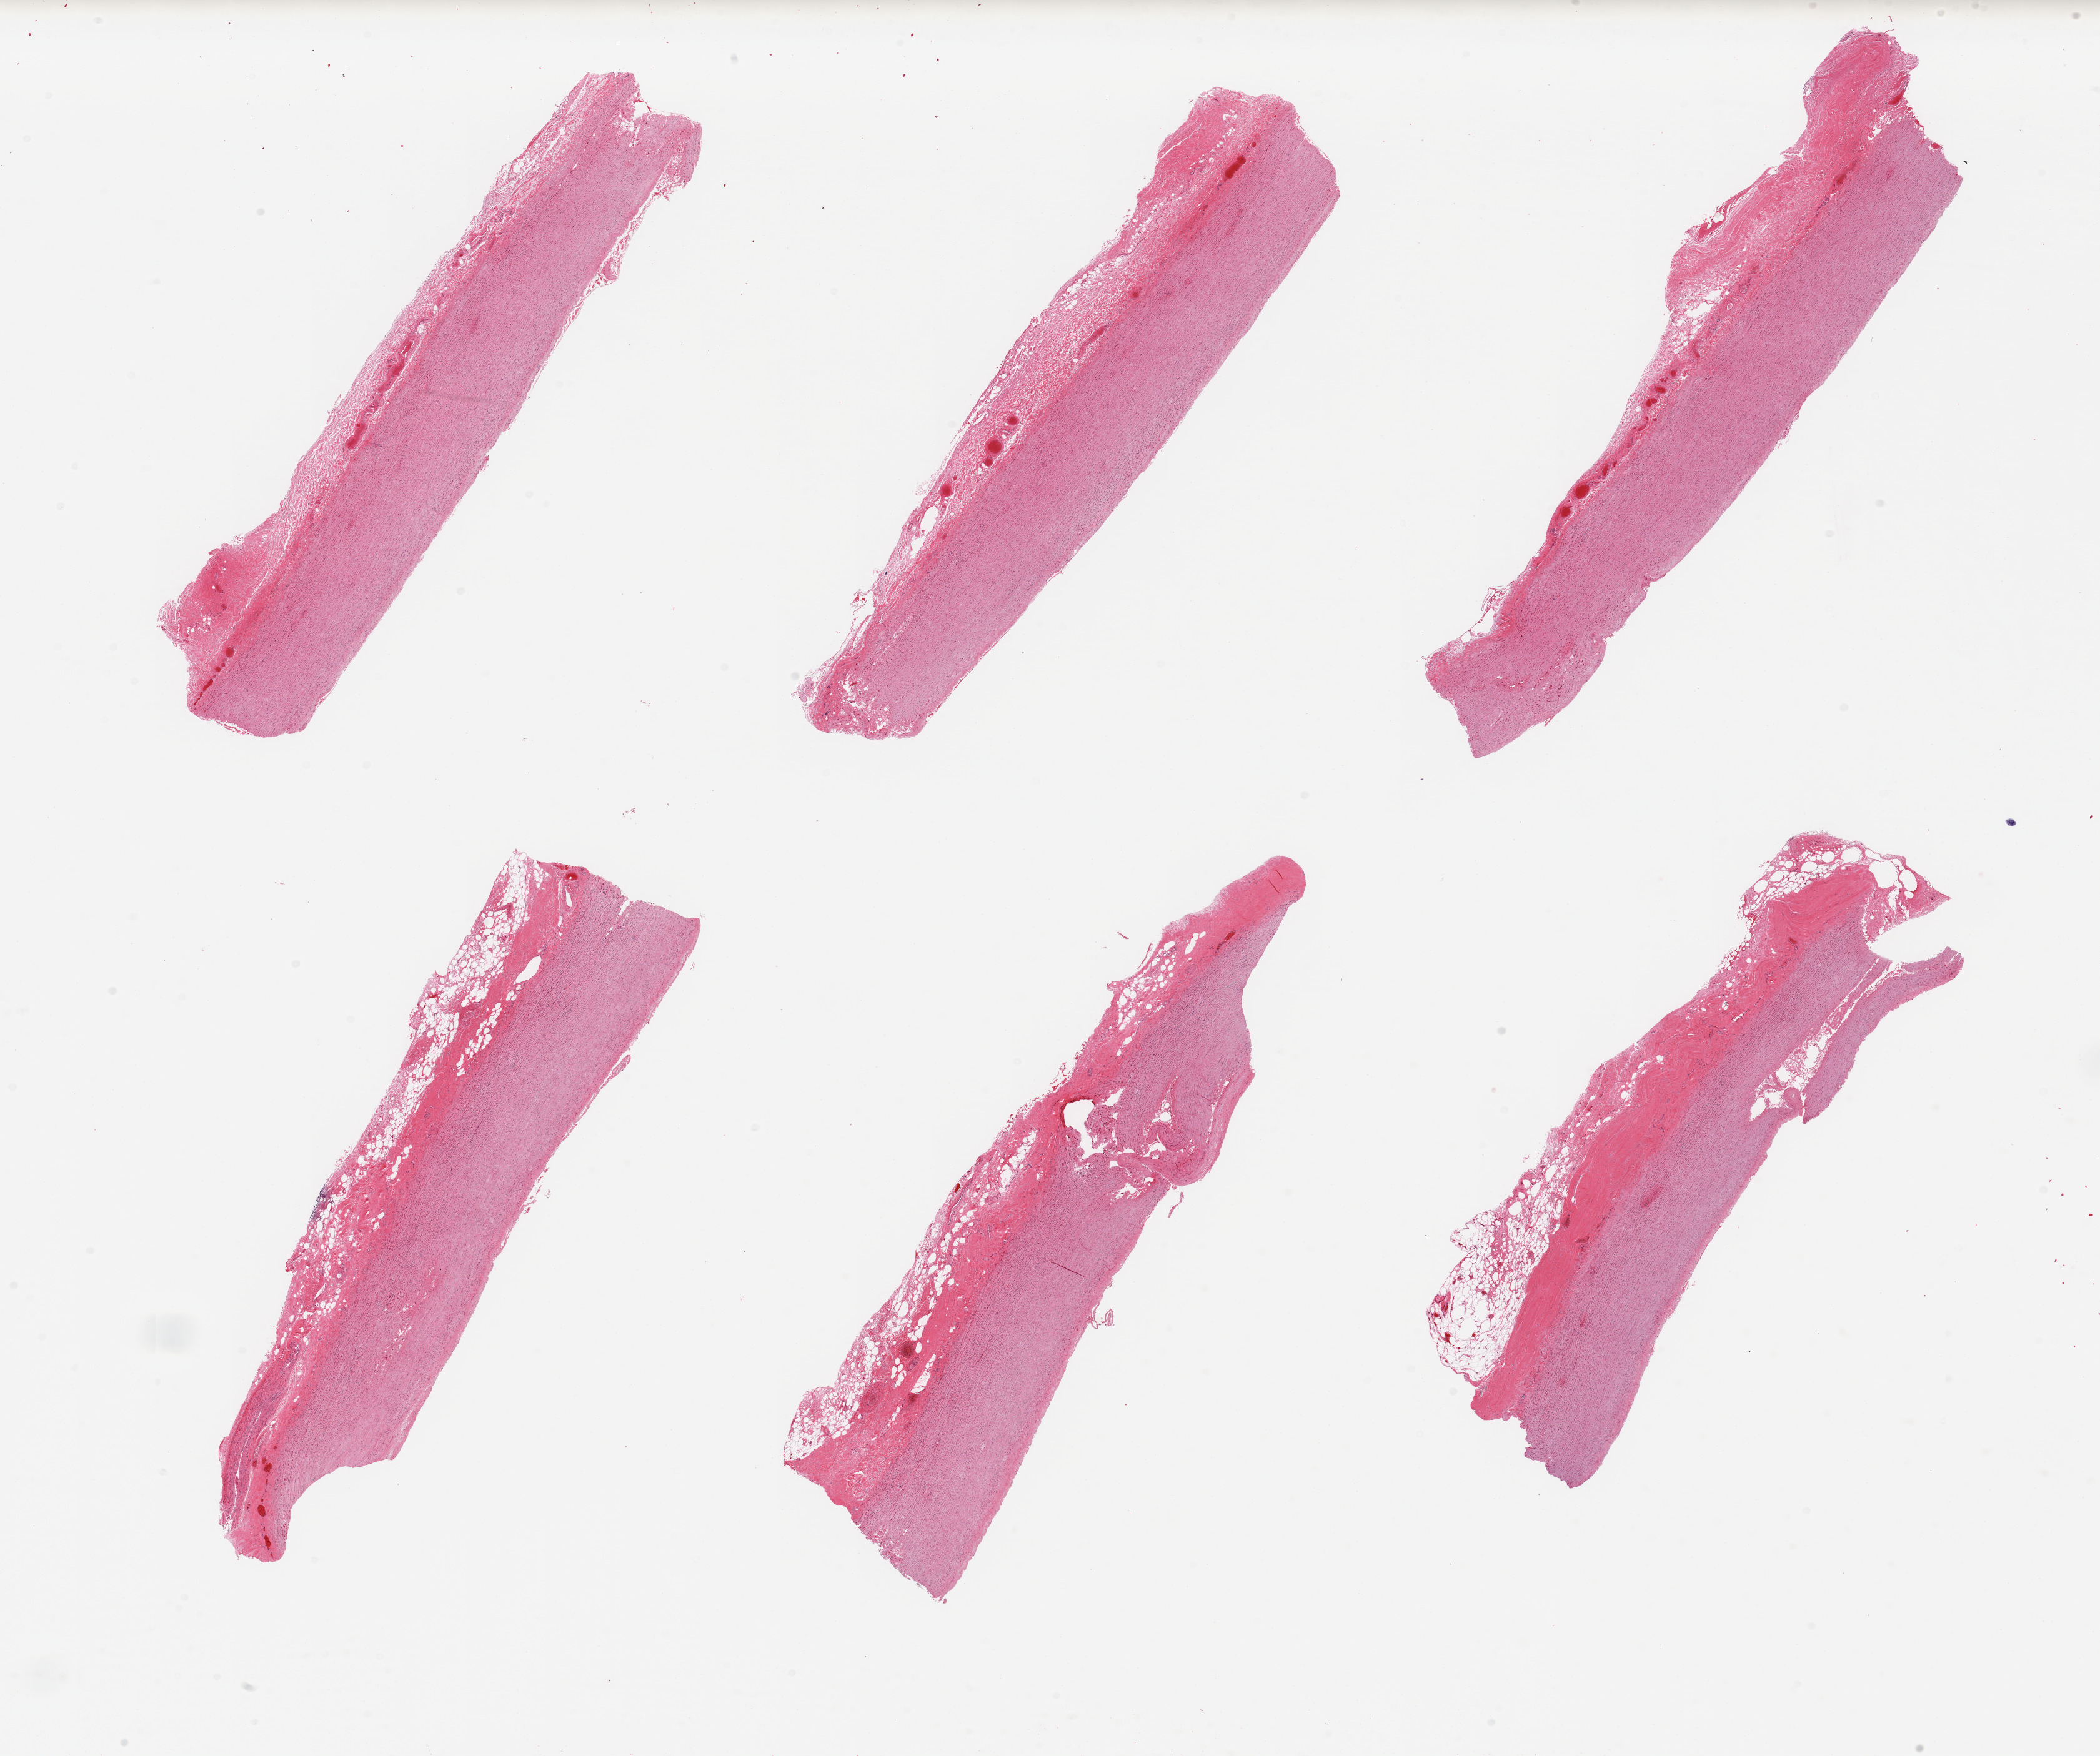
Digitized hematoxylin and eosin (H&E)-stained section — low-resolution overview of the scanned area, about 26.6 x 22.2 mm. PAXgene-fixed paraffin-embedded (PFPE) section. Section of aorta (target tissue). Tissue donor sample. Donor sex: male.
Review note (as recorded): 6 pieces, adherent serosa/fat up to ~1.5mm.